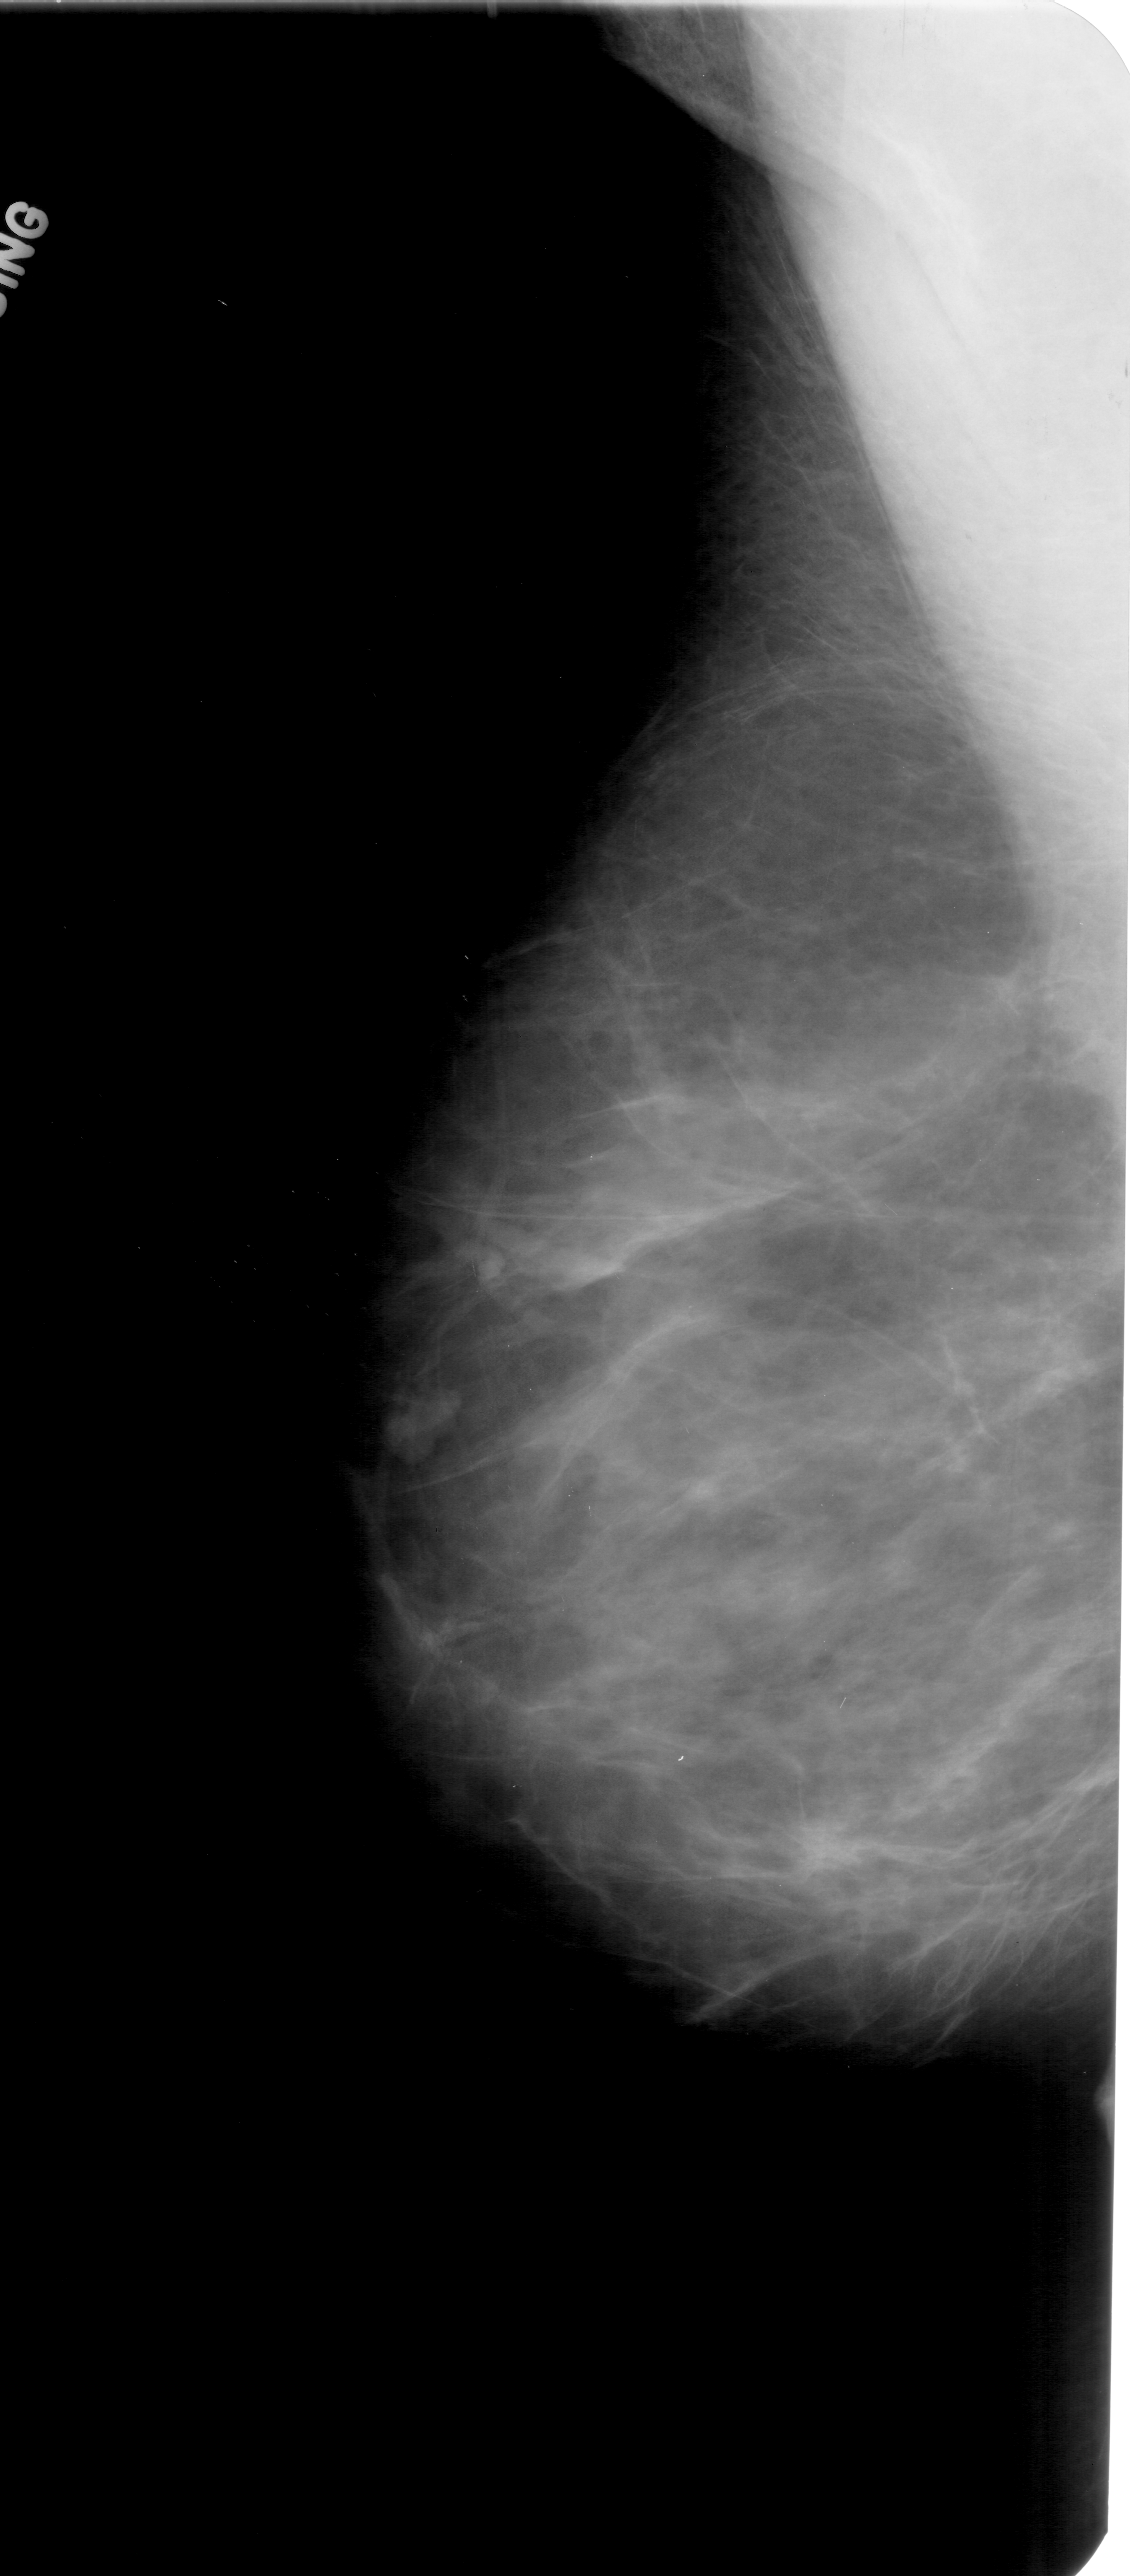
Mammogram (digitized film), left breast, MLO view.
Abnormality record for this image: mass, shape lobulated, margins circumscribed; BI-RADS assessment category 4; subtlety rating 3 on a 1 (subtle) to 5 (obvious) scale; pathology result (as recorded, not read from the image): benign.